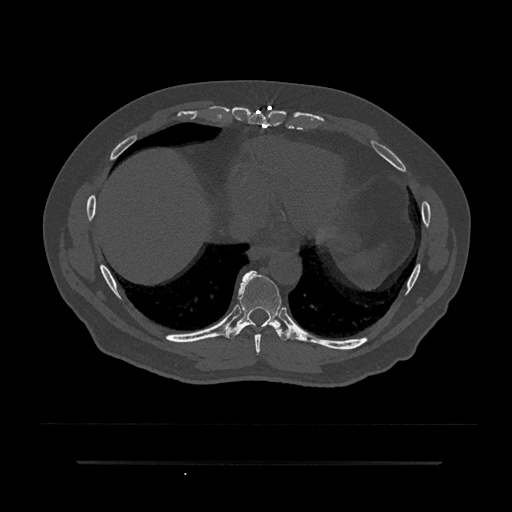
CT including the spine, one axial slice; reconstruction kernel Br40s/3; 120 kVp; bone window (W 1800 / L 400 HU); 0.5 mm slice thickness; 512 × 512 image matrix. Patient: male, 59 years. From the clinical record (not read from this slice): primary cancer: bile ducts; vertebrae with lytic lesions (as recorded): T10.
Annotated regions visible in this slice (semi-automatic segmentation, software-assisted and operator-edited):
- T8 vertebra: bounding box [x1, y1, x2, y2] px = [254, 334, 261, 355]
- T9 vertebra: [227, 271, 289, 341]